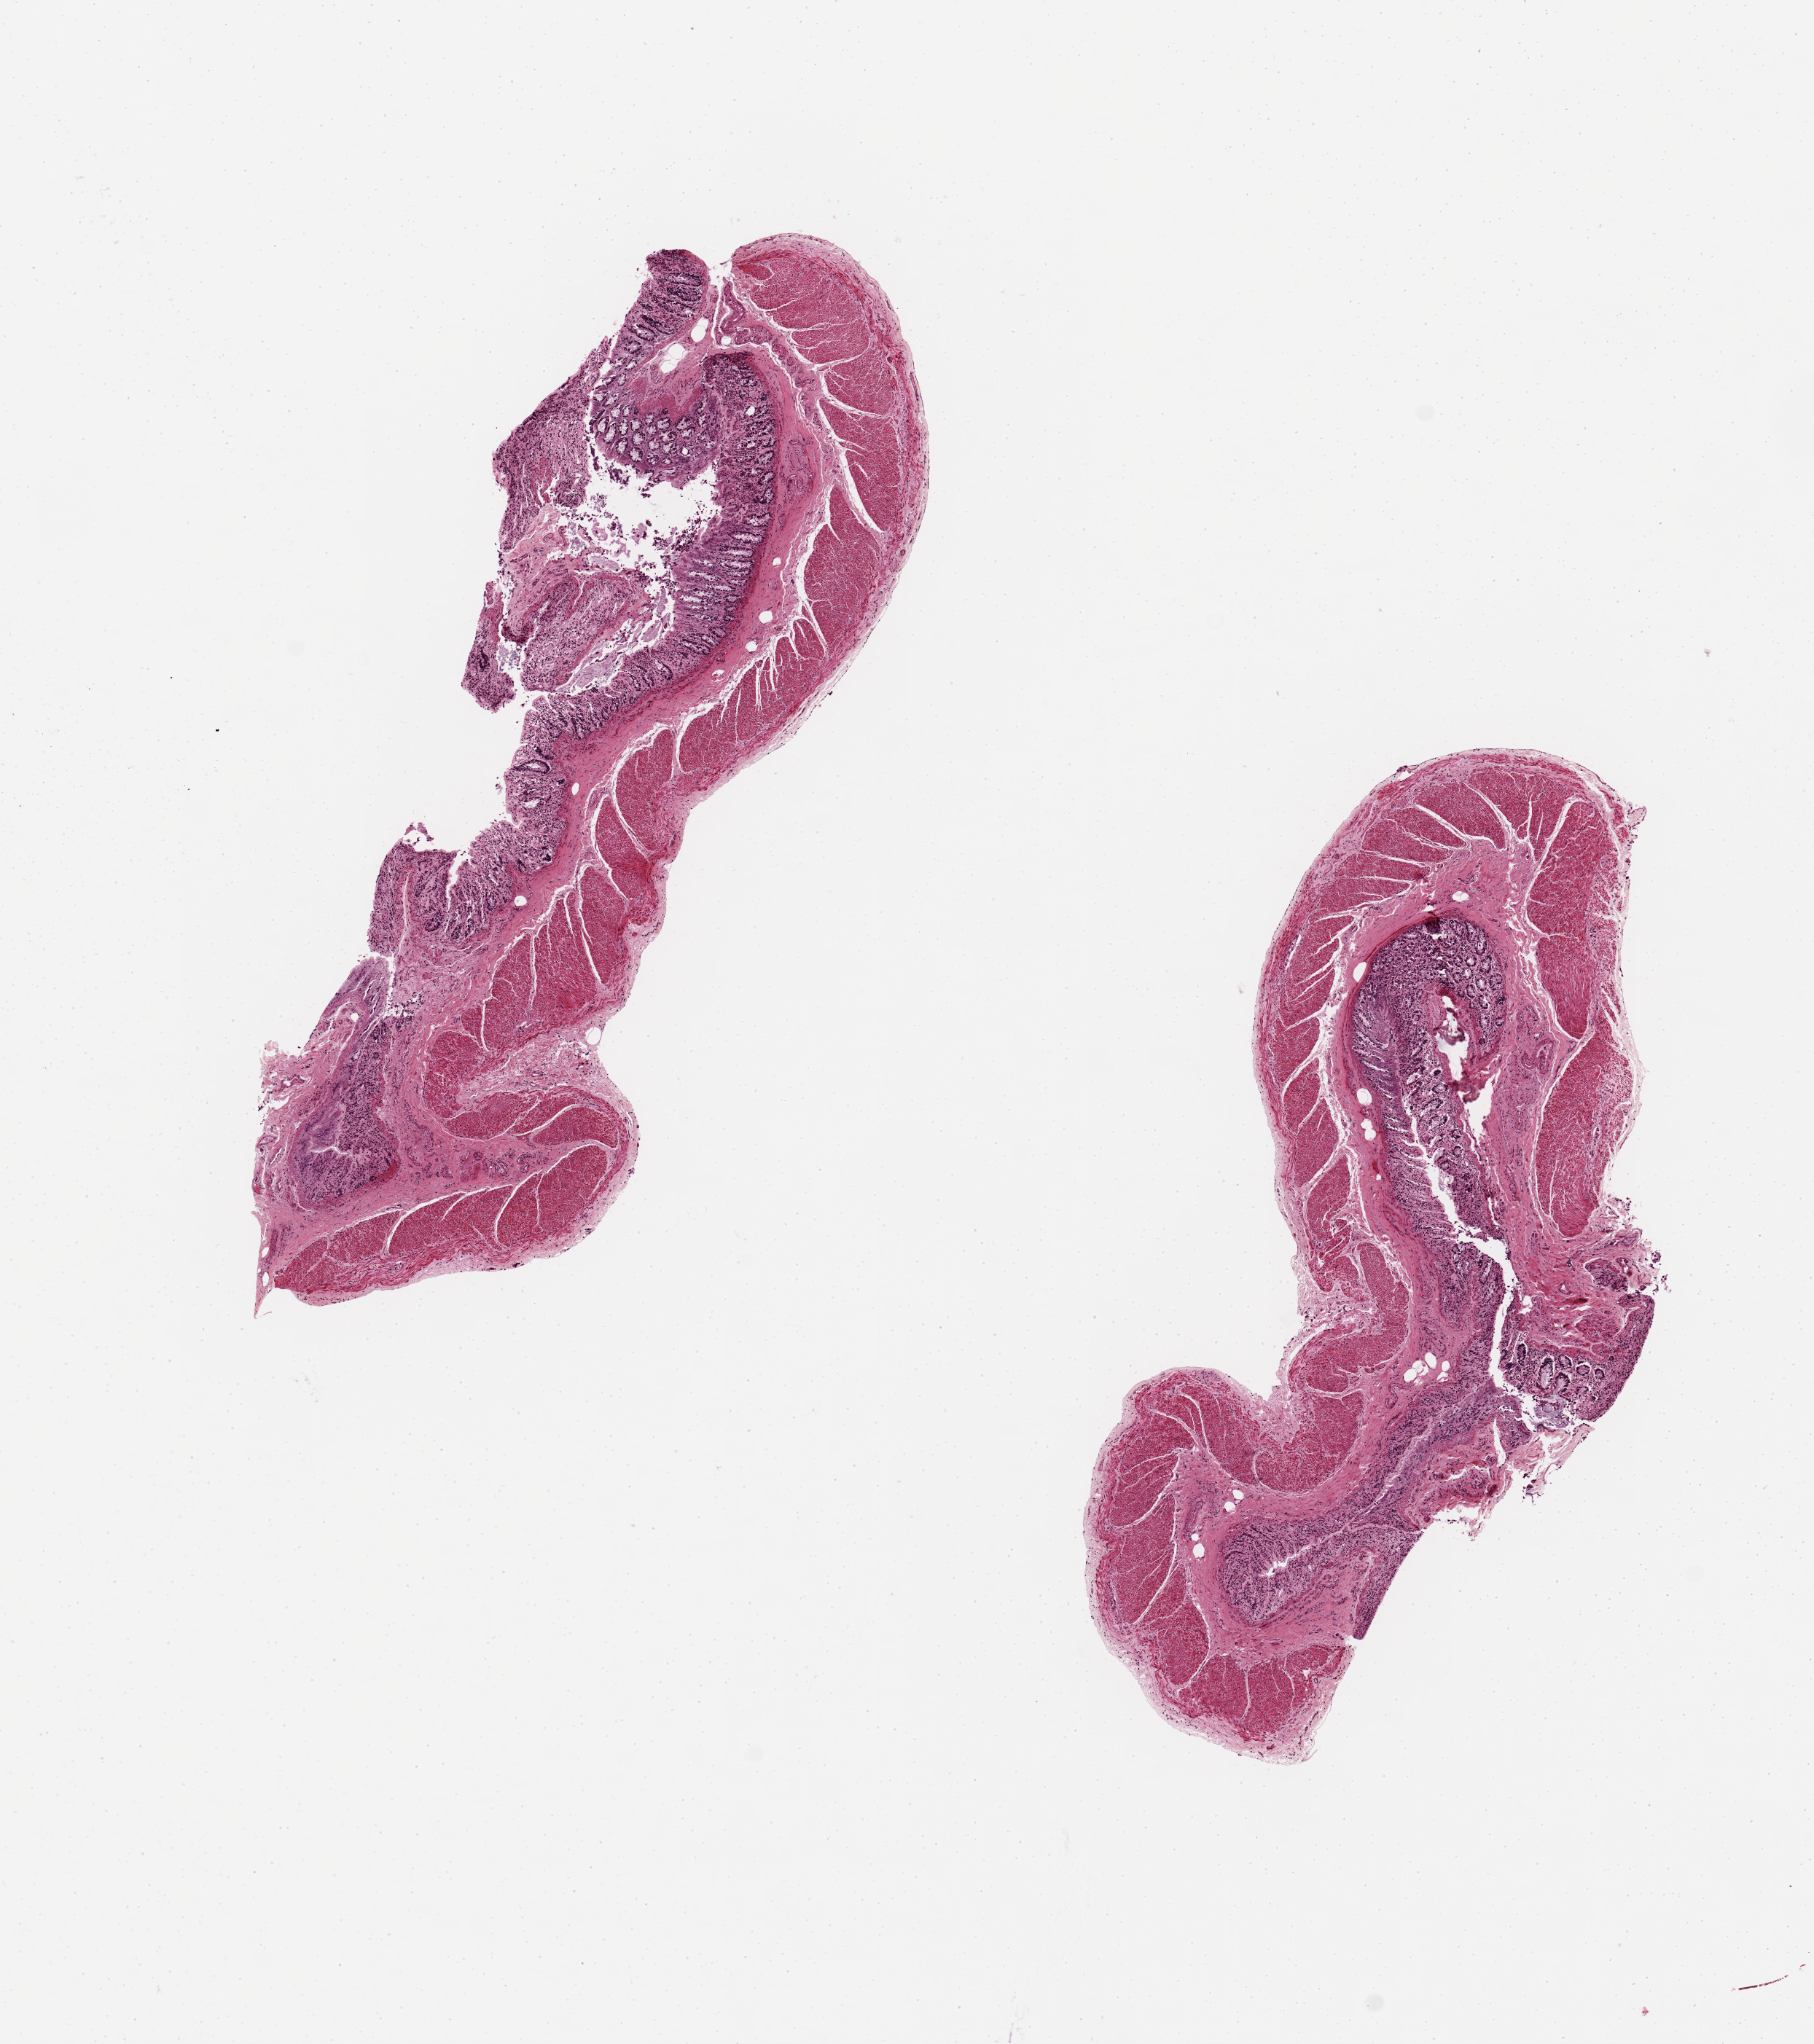
Whole-slide image, haematoxylin and eosin stain — whole scanned area (about 9.8 x 11.1 mm) shown as a low-resolution overview, PAXgene-fixed paraffin-embedded (PFPE) section, section of transverse colon (target tissue), donor tissue sample. Donor: female.
Pathologist's review note for this sample: 2 pieces, 6x1mm. Epithelium with near-total autolysis.